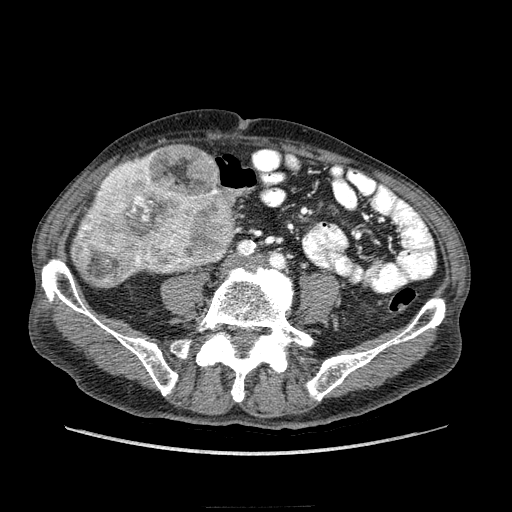
Contrast-enhanced abdominal CT (liver protocol), one axial slice. Position 33 of 218 along the scan axis. Soft-tissue window (W 400 / L 40 HU). 2.5 mm slice thickness. 512 × 512 image matrix. Case-level facts recorded for this patient, not image findings: diagnosis: hepatocellular carcinoma (patient treated with transarterial chemoembolisation; whether this scan precedes or follows treatment is not stated here); TNM stage (as recorded): Stage-IIIA; Child-Pugh class: A; tumour differentiation: well differentiated; tumour nodularity: multinodular.
Structures marked on this image (semi-automatic segmentation, software-assisted and operator-edited):
- liver parenchyma outside the tumour (the mass and vessels are separate outlines, so this box may not span the whole liver): bounding box (x1, y1, x2, y2) in pixels: (106, 174, 109, 177)
- mass: (70, 144, 240, 288)